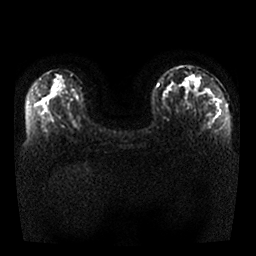
Breast MRI, one axial slice. Slice 15 of 25 in the series (ordered by position). Diffusion-weighted series; image 2 of 4 stored at this slice position (different b-values; order by instance number). 1.5 T. 4 mm slice thickness. 256 × 256 image matrix. Female patient.
Annotated regions visible in this slice (manually delineated by an expert):
- tumour on diffusion-weighted imaging: bounding box (x1, y1, x2, y2) in pixels: (187, 73, 201, 88)